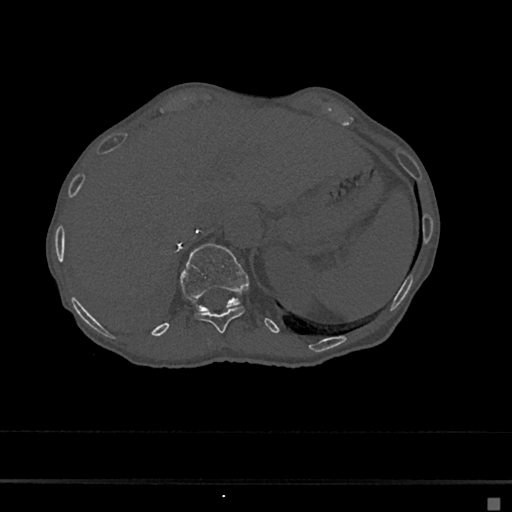
CT including the spine, one axial slice. Position 153 of 797 along the scan axis. Reconstruction kernel Br40s/3. 120 kVp. Bone window (W 1800 / L 400 HU). 0.5 mm slice thickness. 512 × 512 image matrix, field of view 360 × 360 mm. Patient: female, 68 years. Case-level facts recorded for this patient, not image findings: primary cancer: renal.
Outlined on this slice (semi-automatic segmentation, software-assisted and operator-edited):
- T11 vertebra: bounding box <195,306,245,333> (left, top, right, bottom; pixels)
- T12 vertebra: <179,243,248,312>